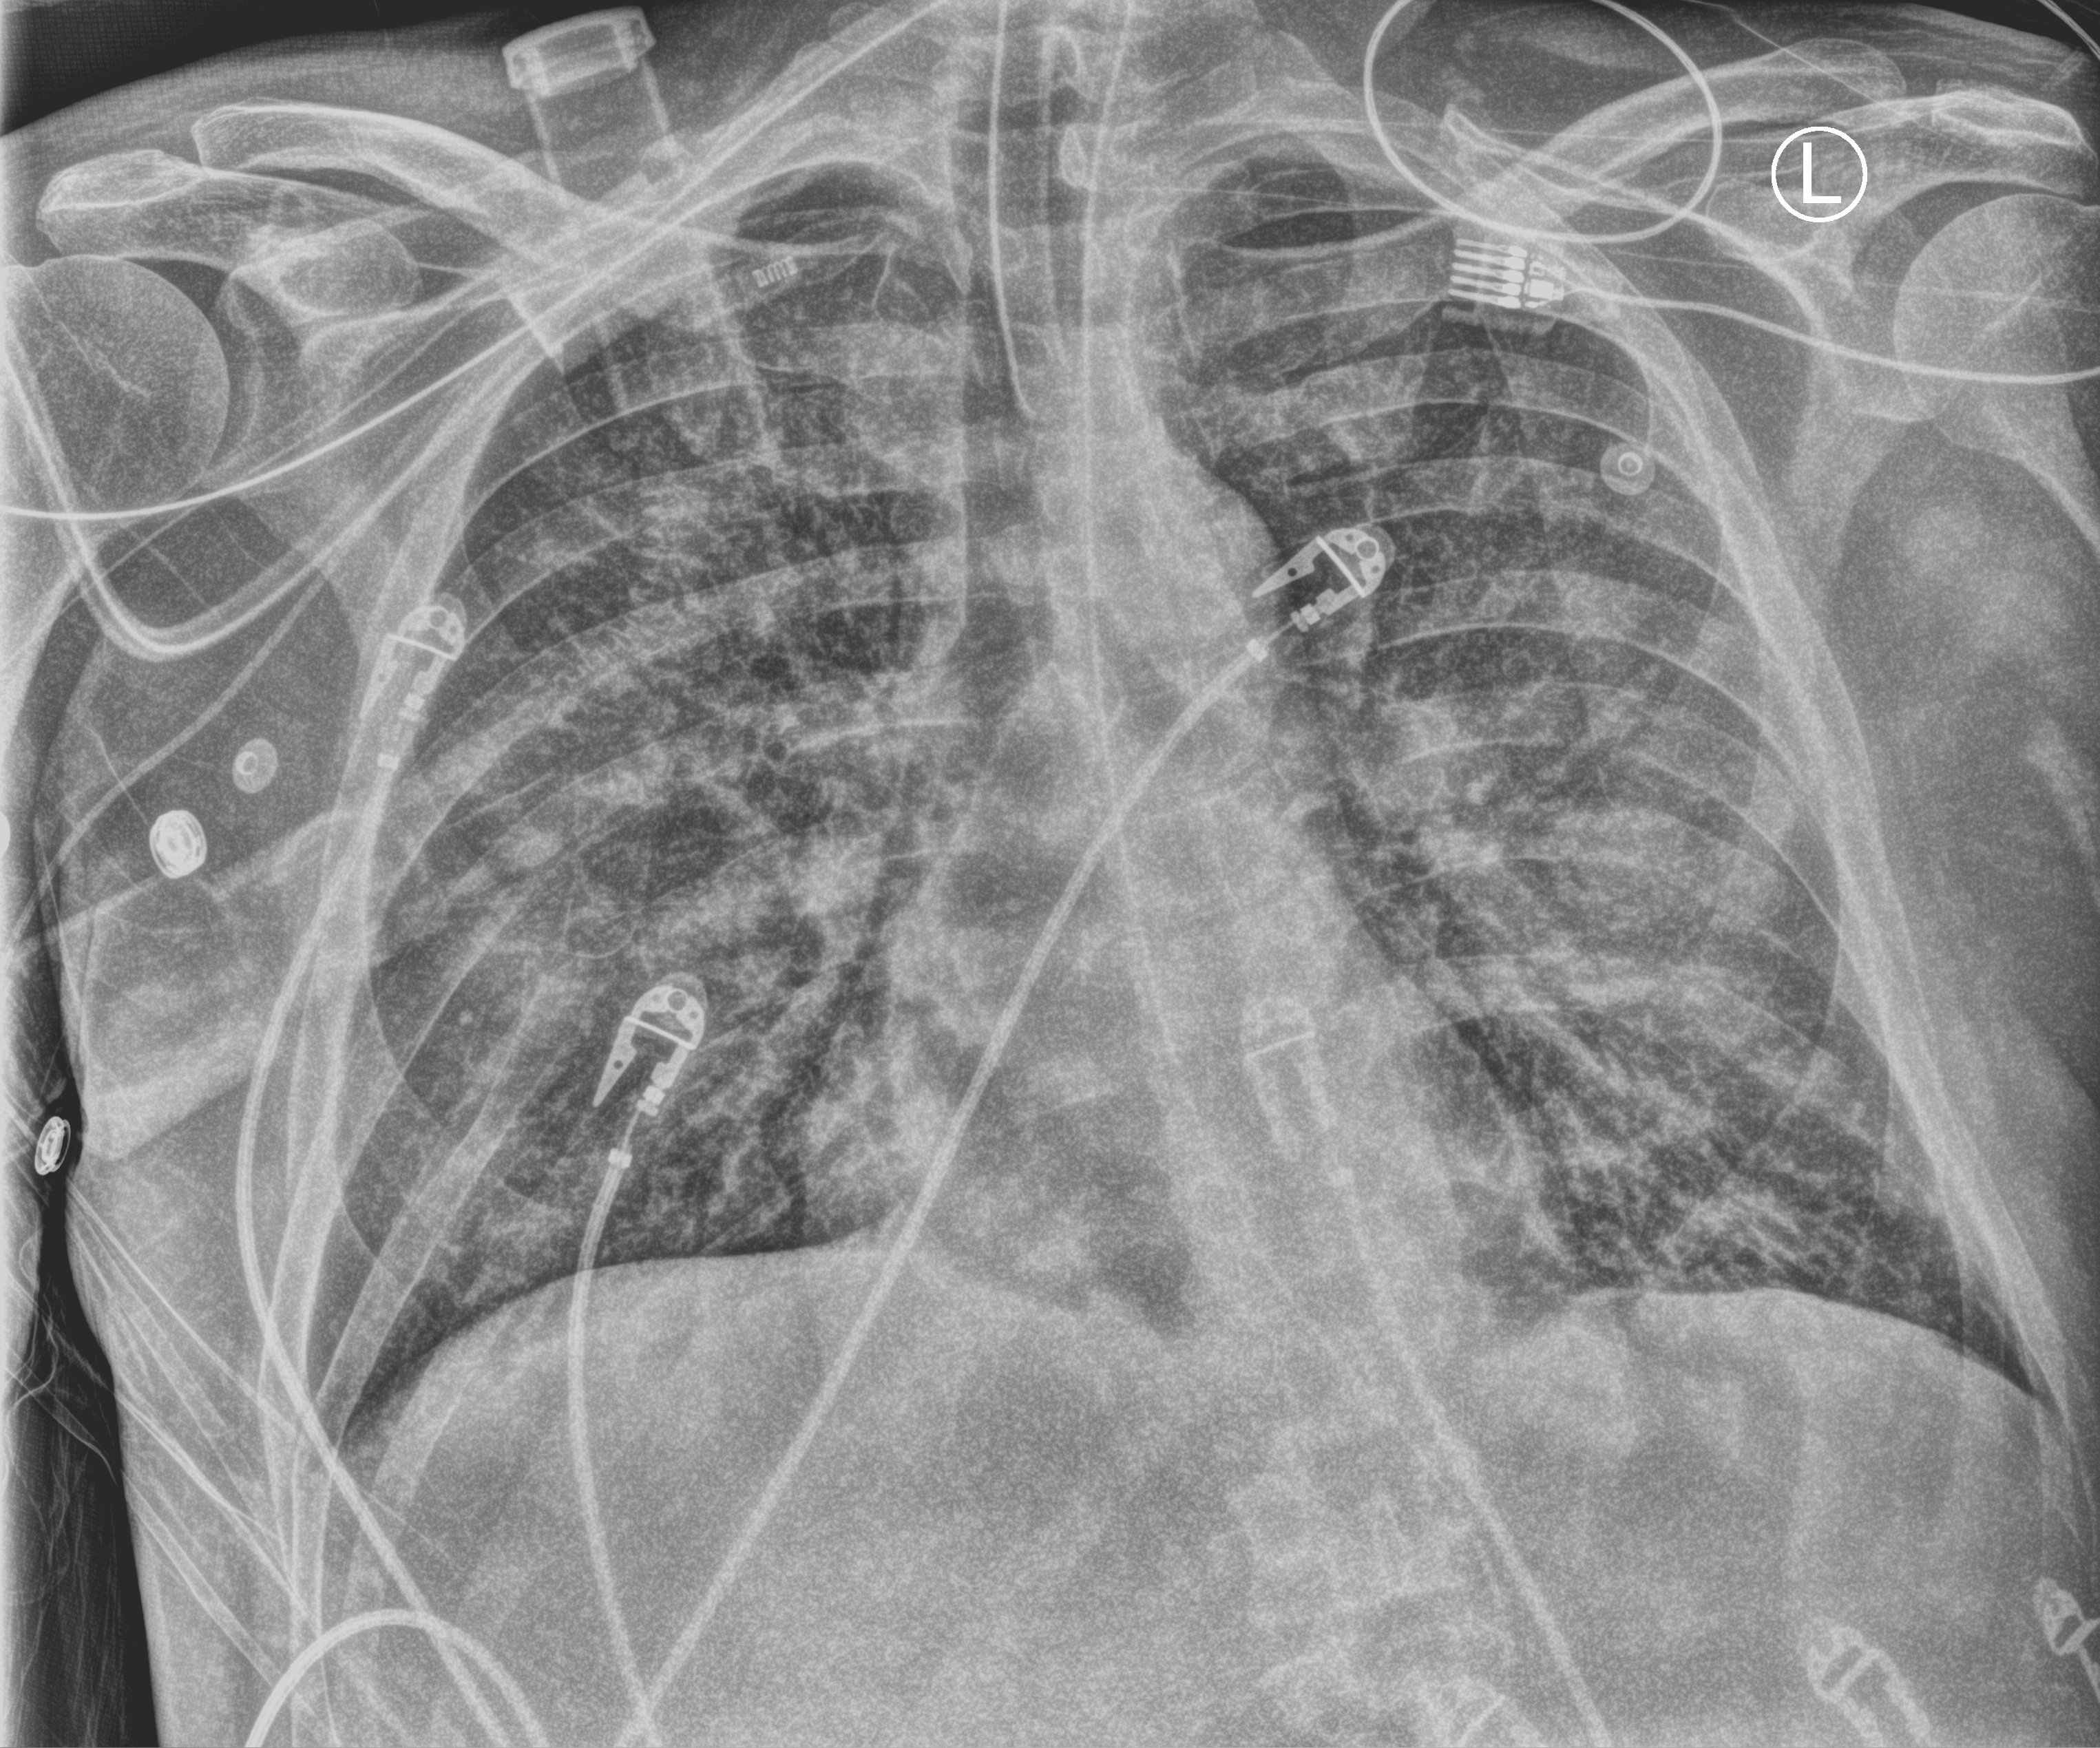
Chest X-ray (portable), anteroposterior (AP) projection. Male patient hospitalised with COVID-19, age 18–59 years.
Admission-level facts for this patient (not findings on this image; timing relative to this image not recorded):
- admitted to intensive care during this hospital stay: yes
- other chronic lung disease (admission record): no
- mechanically ventilated during this hospital stay: yes